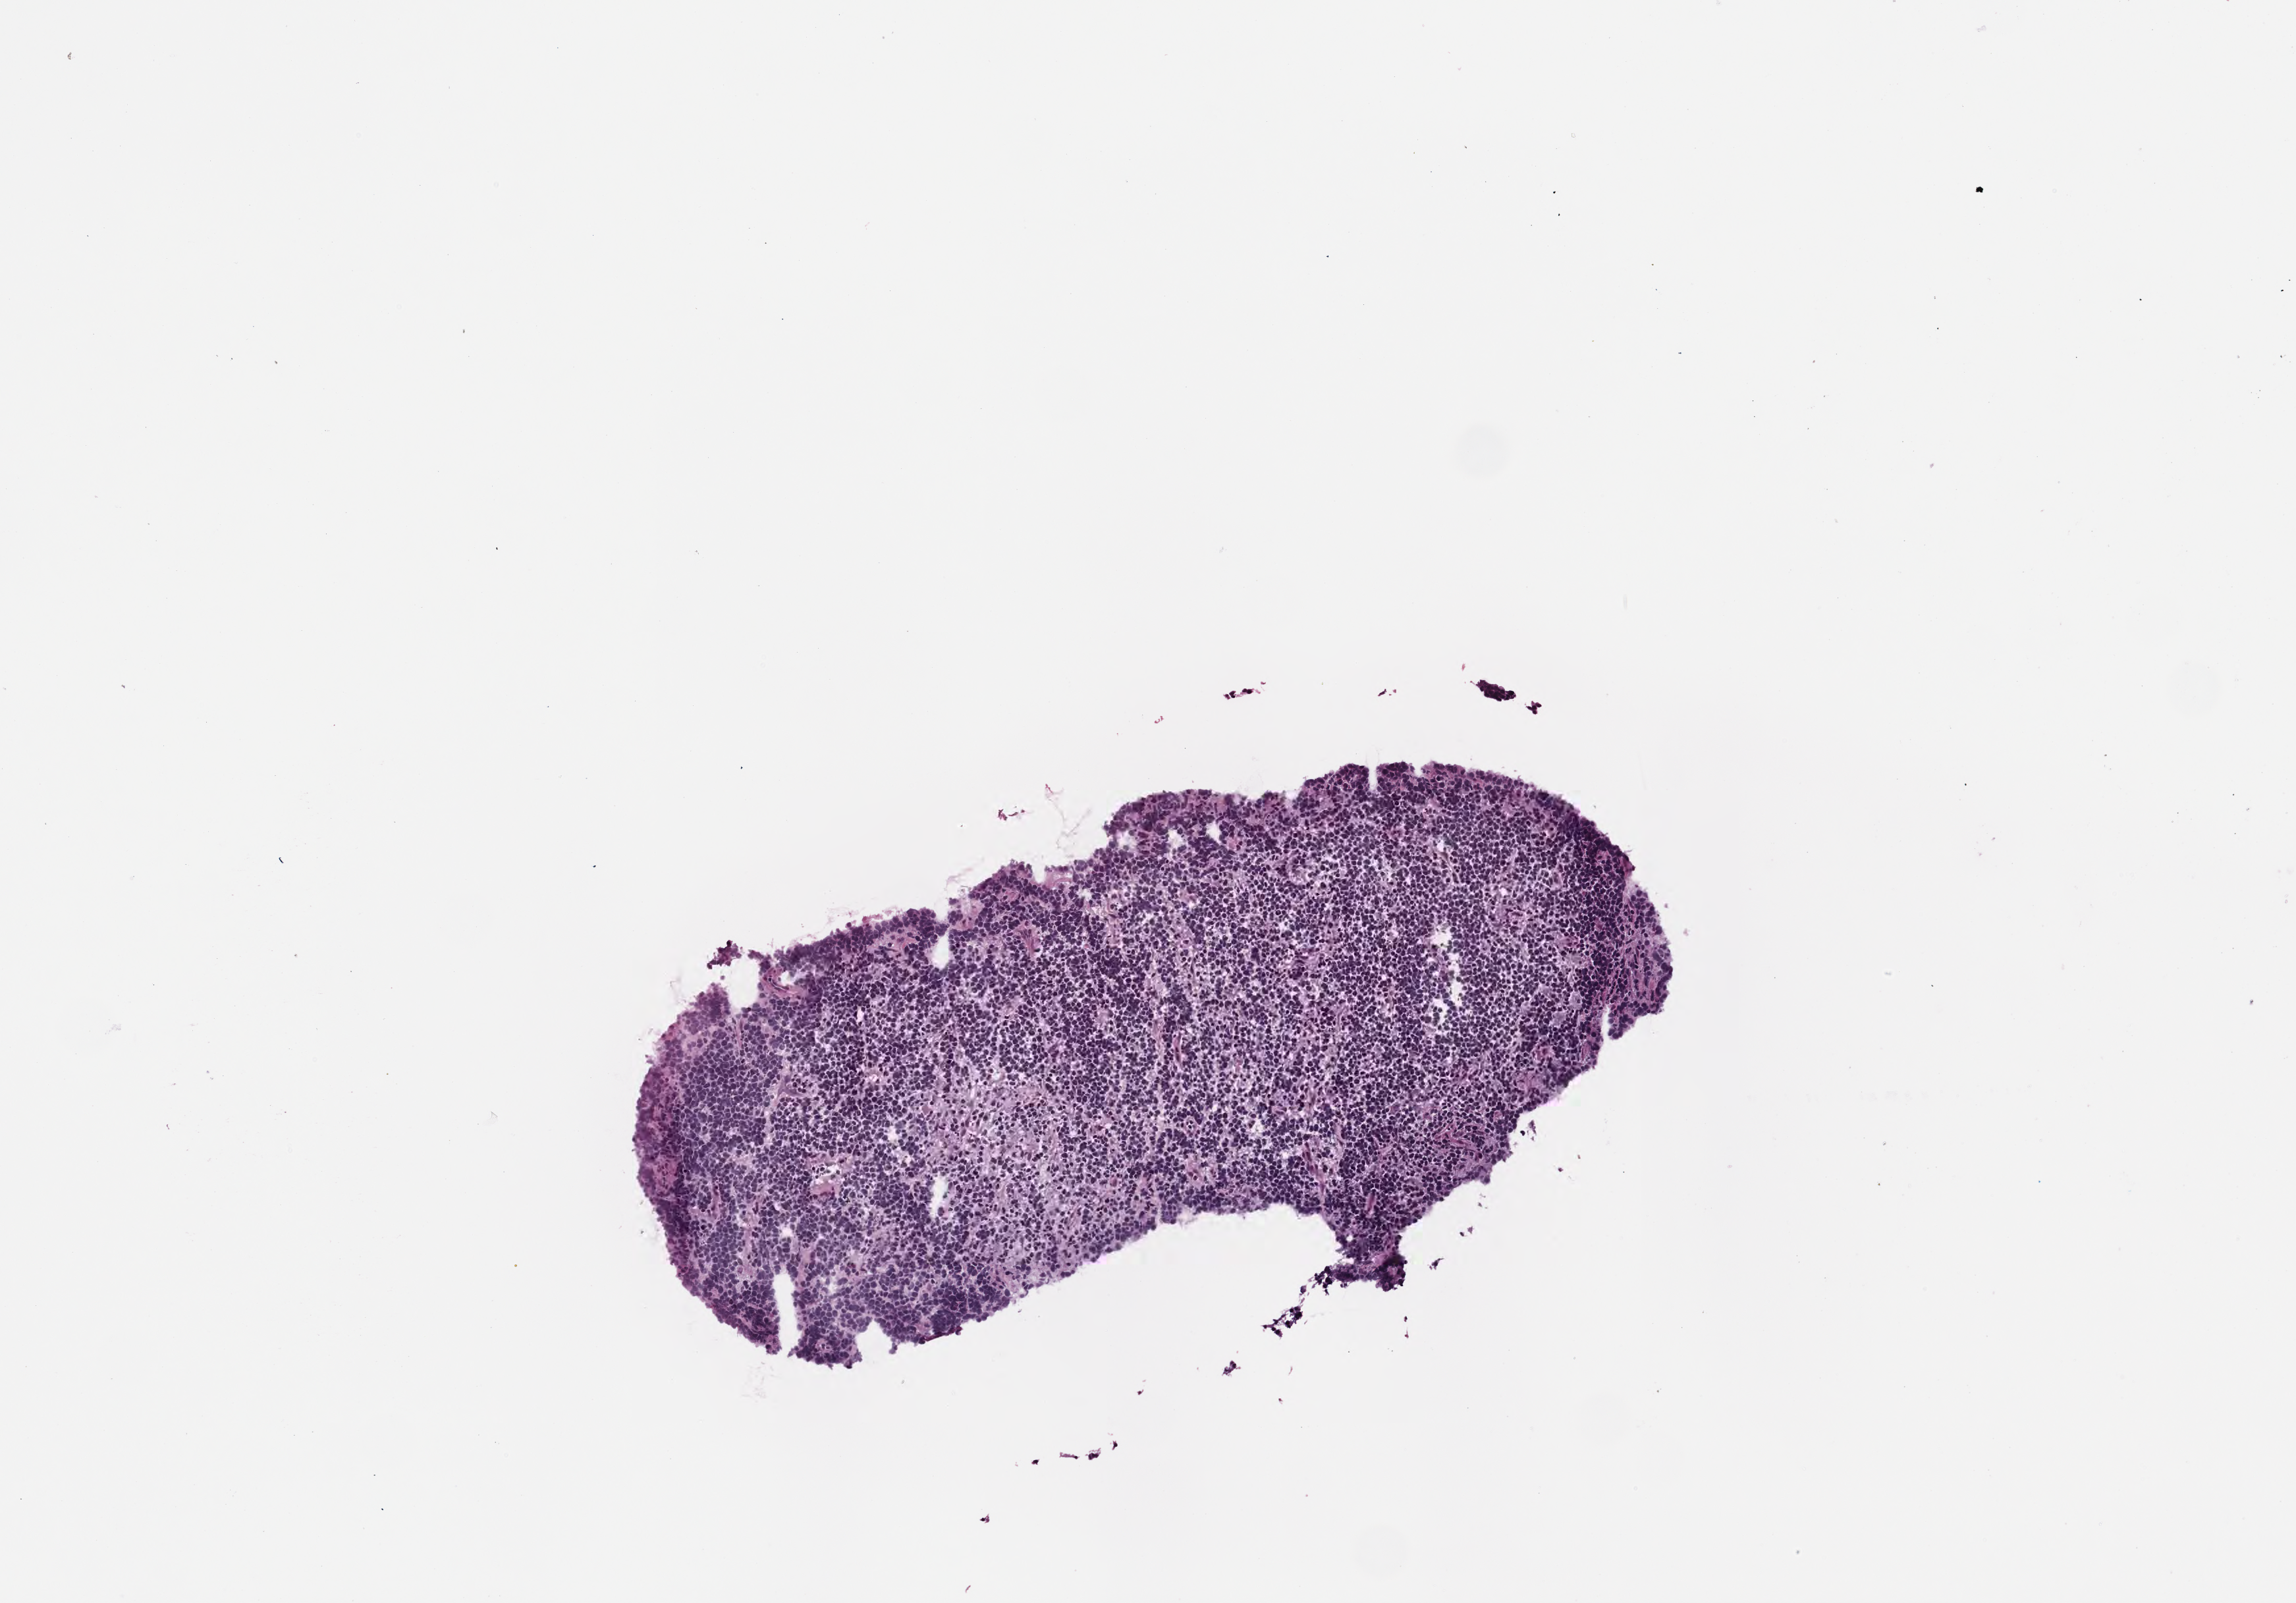
Whole-slide image, haematoxylin and eosin stain, low-resolution overview of the scanned area, about 3.5 x 2.5 mm. Patient sex: male. Composition of this section per pathologist review: tumor cells 85%, tumor nuclei 90%, stromal cells 5%, necrosis 10%, normal cells 0%. Inflammatory infiltration, as recorded: lymphocyte infiltration 20%, monocyte infiltration 30%, neutrophil infiltration 10%.
• specimen: frozen section; primary tumor; anatomic site: liver